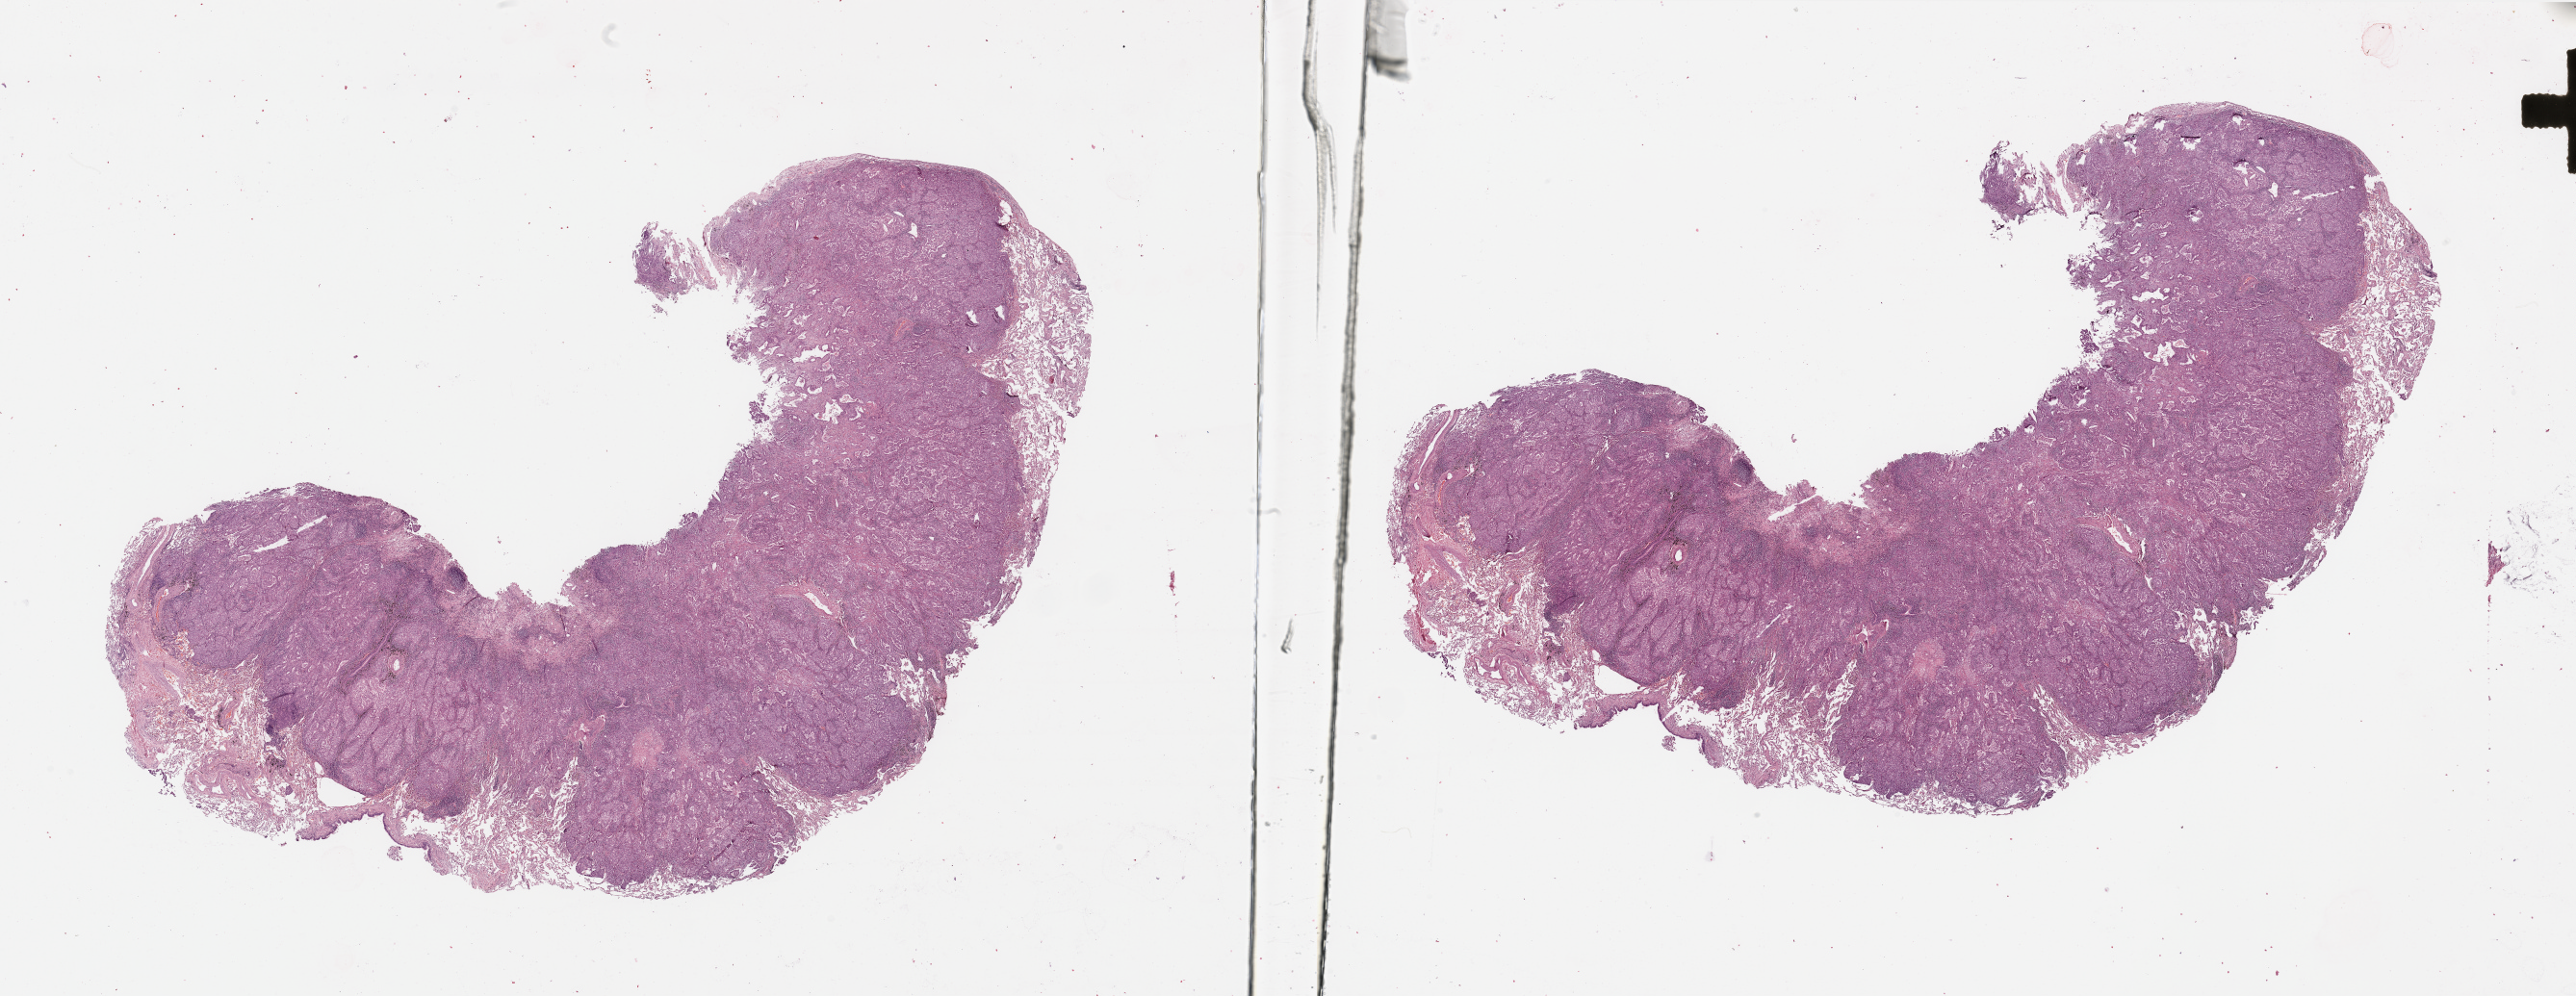
H&E whole-slide image, shown as a low-resolution overview of the whole scanned area (about 42.3 x 16.4 mm, acquisition: 20x scan). Tumour tissue sample, sampled site: lung. Patient: male, age 54 years. Histologic grade: G2 (moderately differentiated). Pathologist review of this section (percent, as recorded): tumour nuclei 80%, necrosis 2%.
• AJCC pathologic stage: IB
• histologic diagnosis: Adenocarcinoma, NOS
• primary tumour site (as recorded): left lower lobe